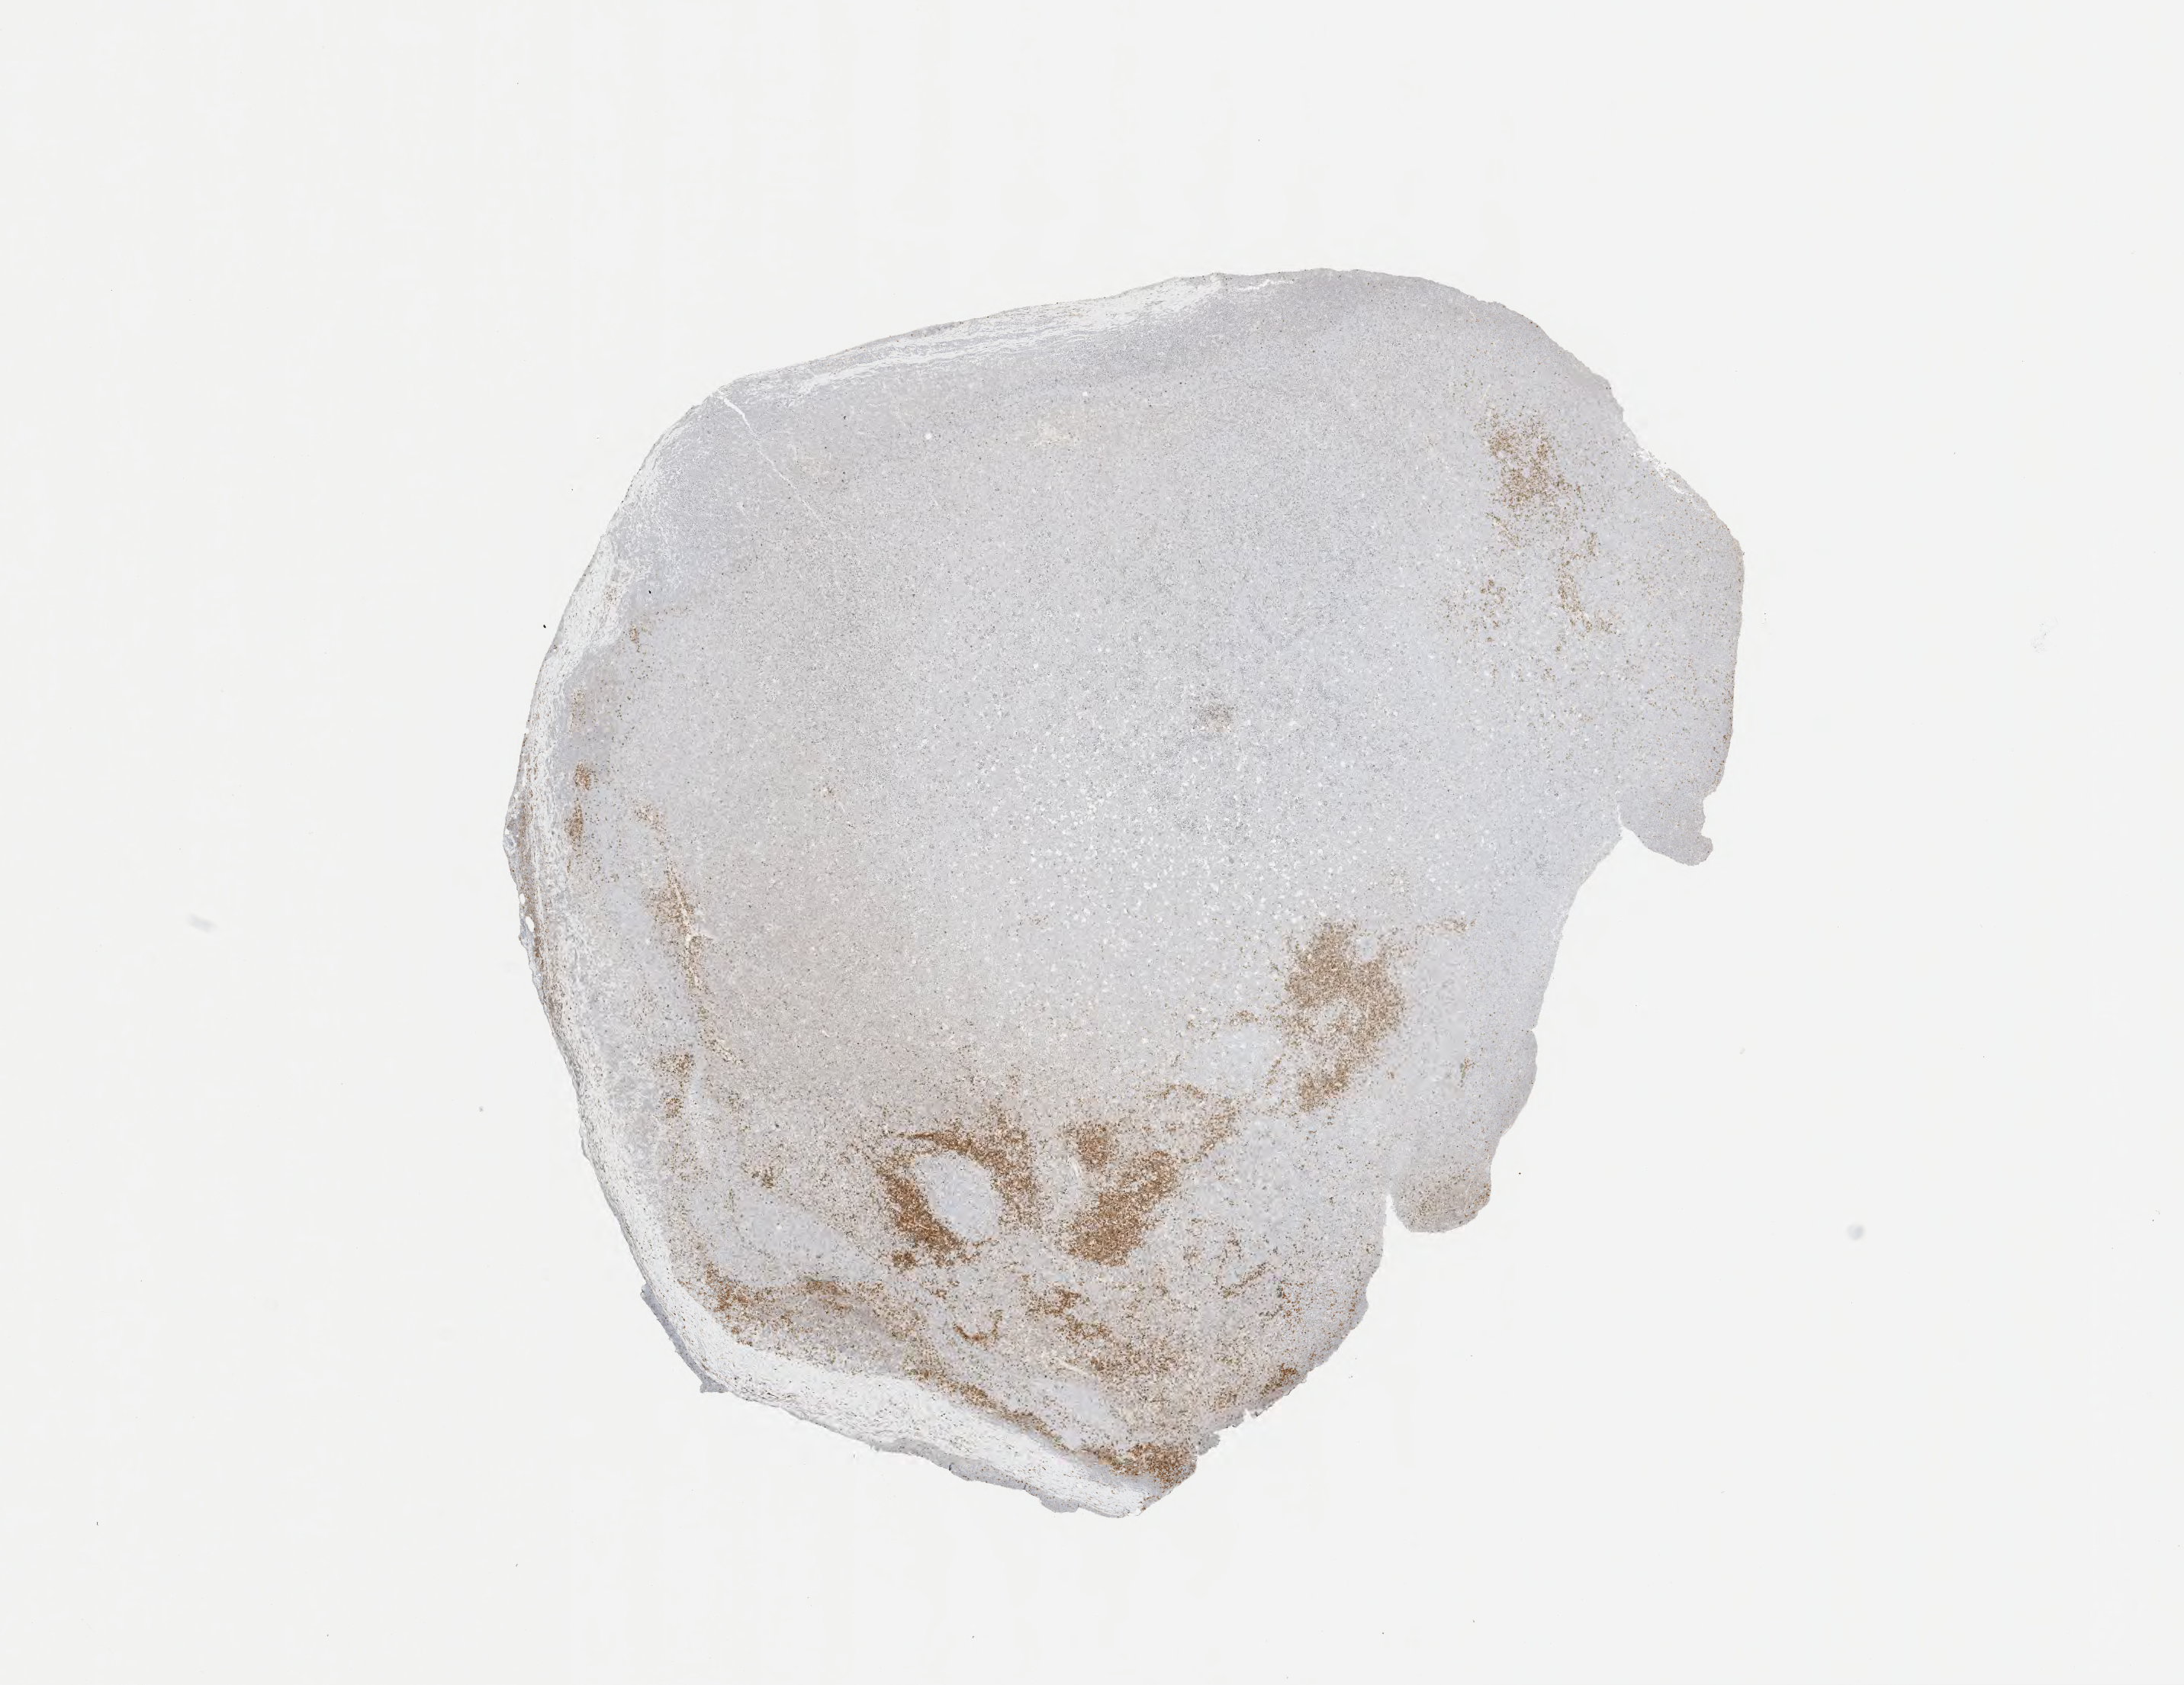
Immunohistochemistry (IHC) whole-slide image stained for BCL2, low-resolution overview of the scanned area, about 11.6 x 8.9 mm, specimen: tumor tissue. Patient: male, 45 years old.
* diagnosis: Burkitt lymphoma, NOS